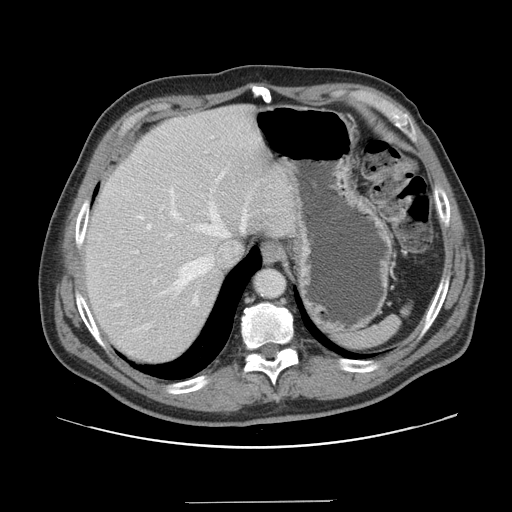
Contrast-enhanced abdominal CT, one axial slice; slice 125 of 151 in the series (ordered by position); 120 kVp; intravenous contrast given; soft-tissue window (W 400 / L 40 HU); 512 × 512 image matrix. Male patient, age 63 years. Case-level facts recorded for this patient, not image findings: diagnosis: colorectal cancer liver metastases, imaged before liver resection; multiple liver metastases: no; largest metastasis: 2.1 cm; disease in both lobes: no.
Structures marked on this image (expert manual segmentation):
- hepatic veins: box from (x=138, y=188) to (x=247, y=302) px
- liver: (x=84, y=106)–(x=298, y=364)
- planned liver remnant (the part of the liver to remain after resection): (x=85, y=119)–(x=253, y=364)
- portal vein (with intrahepatic branches): (x=135, y=206)–(x=164, y=283)